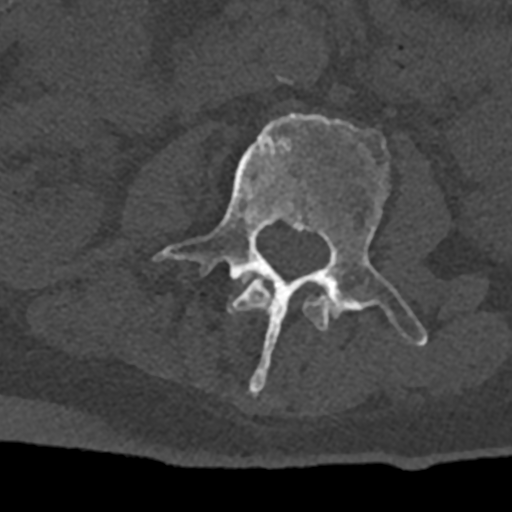
CT including the spine, one axial slice; slice 327 of 797 in the series (ordered by position); reconstruction kernel Br40s/3; bone window (W 1800 / L 400 HU); 0.5 mm slice thickness; 512 × 512 image matrix, field of view 160 × 160 mm. Male patient, age 74 years. From the clinical record (not read from this slice): primary cancer: renal; vertebrae with lytic lesions (as recorded): T10, L1, L2, L3, L4, L5.
Structures marked on this image (semi-automatic segmentation, software-assisted and operator-edited):
- L2 vertebra: box from (x=229, y=280) to (x=329, y=331) px
- L3 vertebra: (x=152, y=113)–(x=428, y=394)